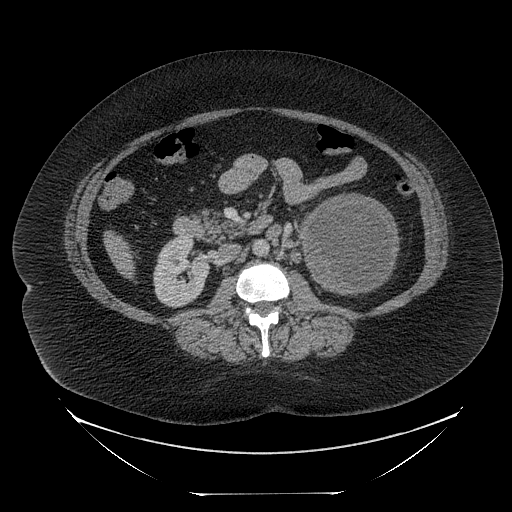
Contrast-enhanced abdominal CT, one axial slice. Slice 119 of 205 in the series (ordered by position). 120 kVp. Intravenous contrast given. Soft-tissue window (W 400 / L 40 HU). 512 × 512 image matrix. Female patient, age 53 years. From the clinical record (not read from this slice): diagnosis: adrenocortical carcinoma; tumour side: left adrenal; tumour size at pathology: 17 cm; Ki-67 index: 20 %; stage (as recorded): 3.
Structures marked on this image (semi-automatically segmented with operator editing):
- mass: bounding box (x1, y1, x2, y2) in pixels: (305, 196, 398, 292)